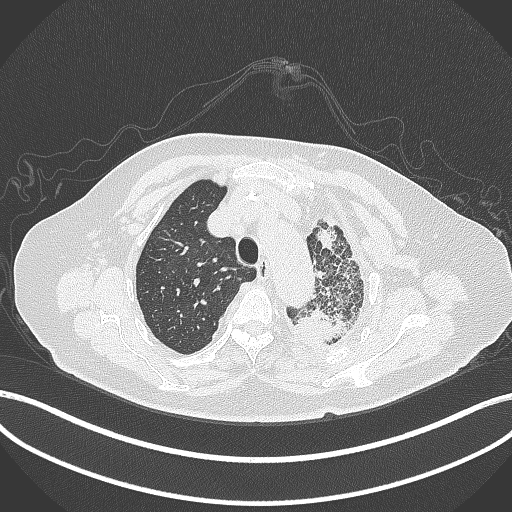
Chest CT, one axial slice; position 311 of 399 along the scan axis; reconstruction kernel B70f; 120 kVp; lung window (W 1500 / L -600 HU); 512 × 512 image matrix, field of view 400 × 400 mm. Female patient, age 75 years. Case-level facts recorded for this patient, not image findings: clinical TNM (as recorded): T3 N3 M1.
Annotated regions visible in this slice (bounding box drawn by a radiologist):
- lung tumour (recorded histology: adenocarcinoma): bounding box [x1, y1, x2, y2] px = [290, 299, 354, 346]